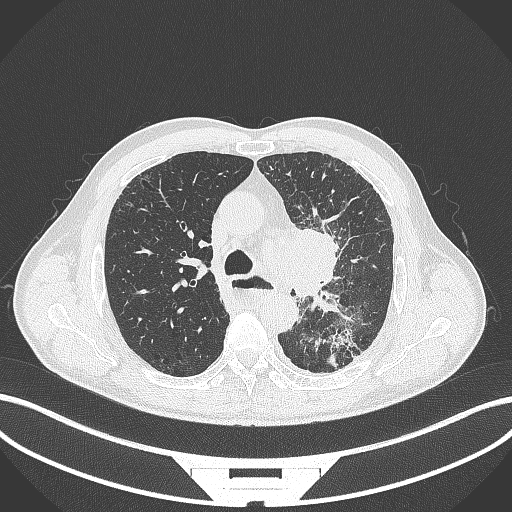
Chest CT, one axial slice. Position 262 of 411 along the scan axis. 120 kVp. Lung window (W 1500 / L -600 HU). 512 × 512 image matrix. Patient: male, 57 years. From the clinical record (not read from this slice): clinical TNM (as recorded): T2a N1 M0.
Annotated regions visible in this slice (rectangle marked by the reading radiologist):
- lung tumour (recorded histology: squamous cell carcinoma): bounding box <287,222,344,306> (left, top, right, bottom; pixels)